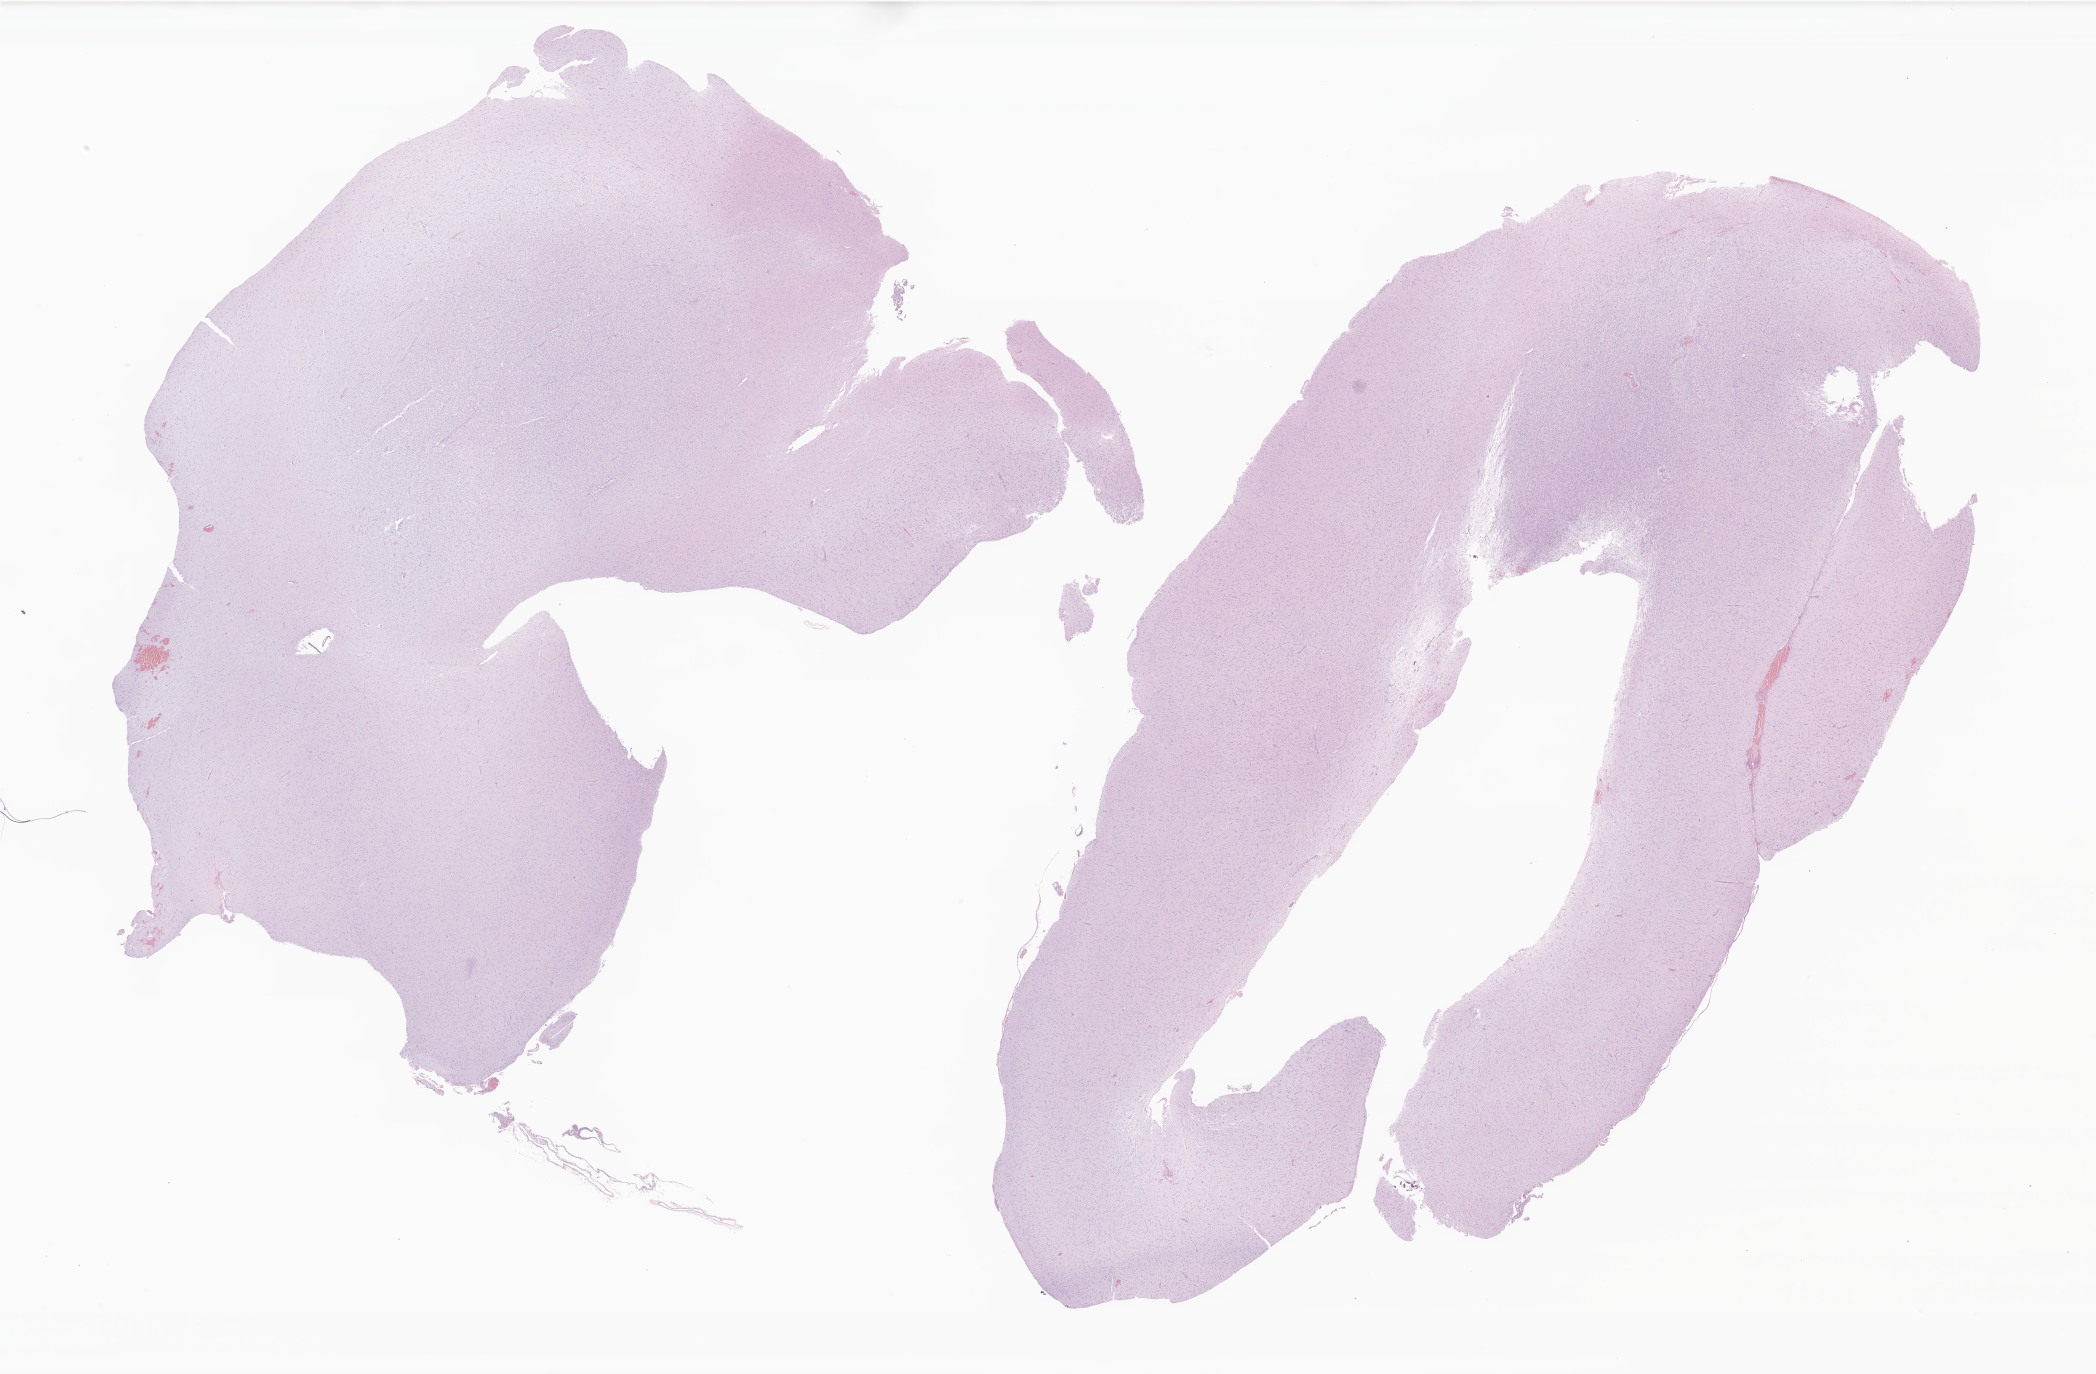
Digitized haematoxylin and eosin-stained section of tumor tissue from the temporal lobe, low-resolution overview of the scanned area, about 35.4 x 23.2 mm, formalin-fixed, paraffin-embedded (FFPE) tissue. Patient: male, age 226 months (18 years 10 months).
Diagnosis (ICD-O-3 morphology term): Dysembryoplastic neuroepithelial tumor.